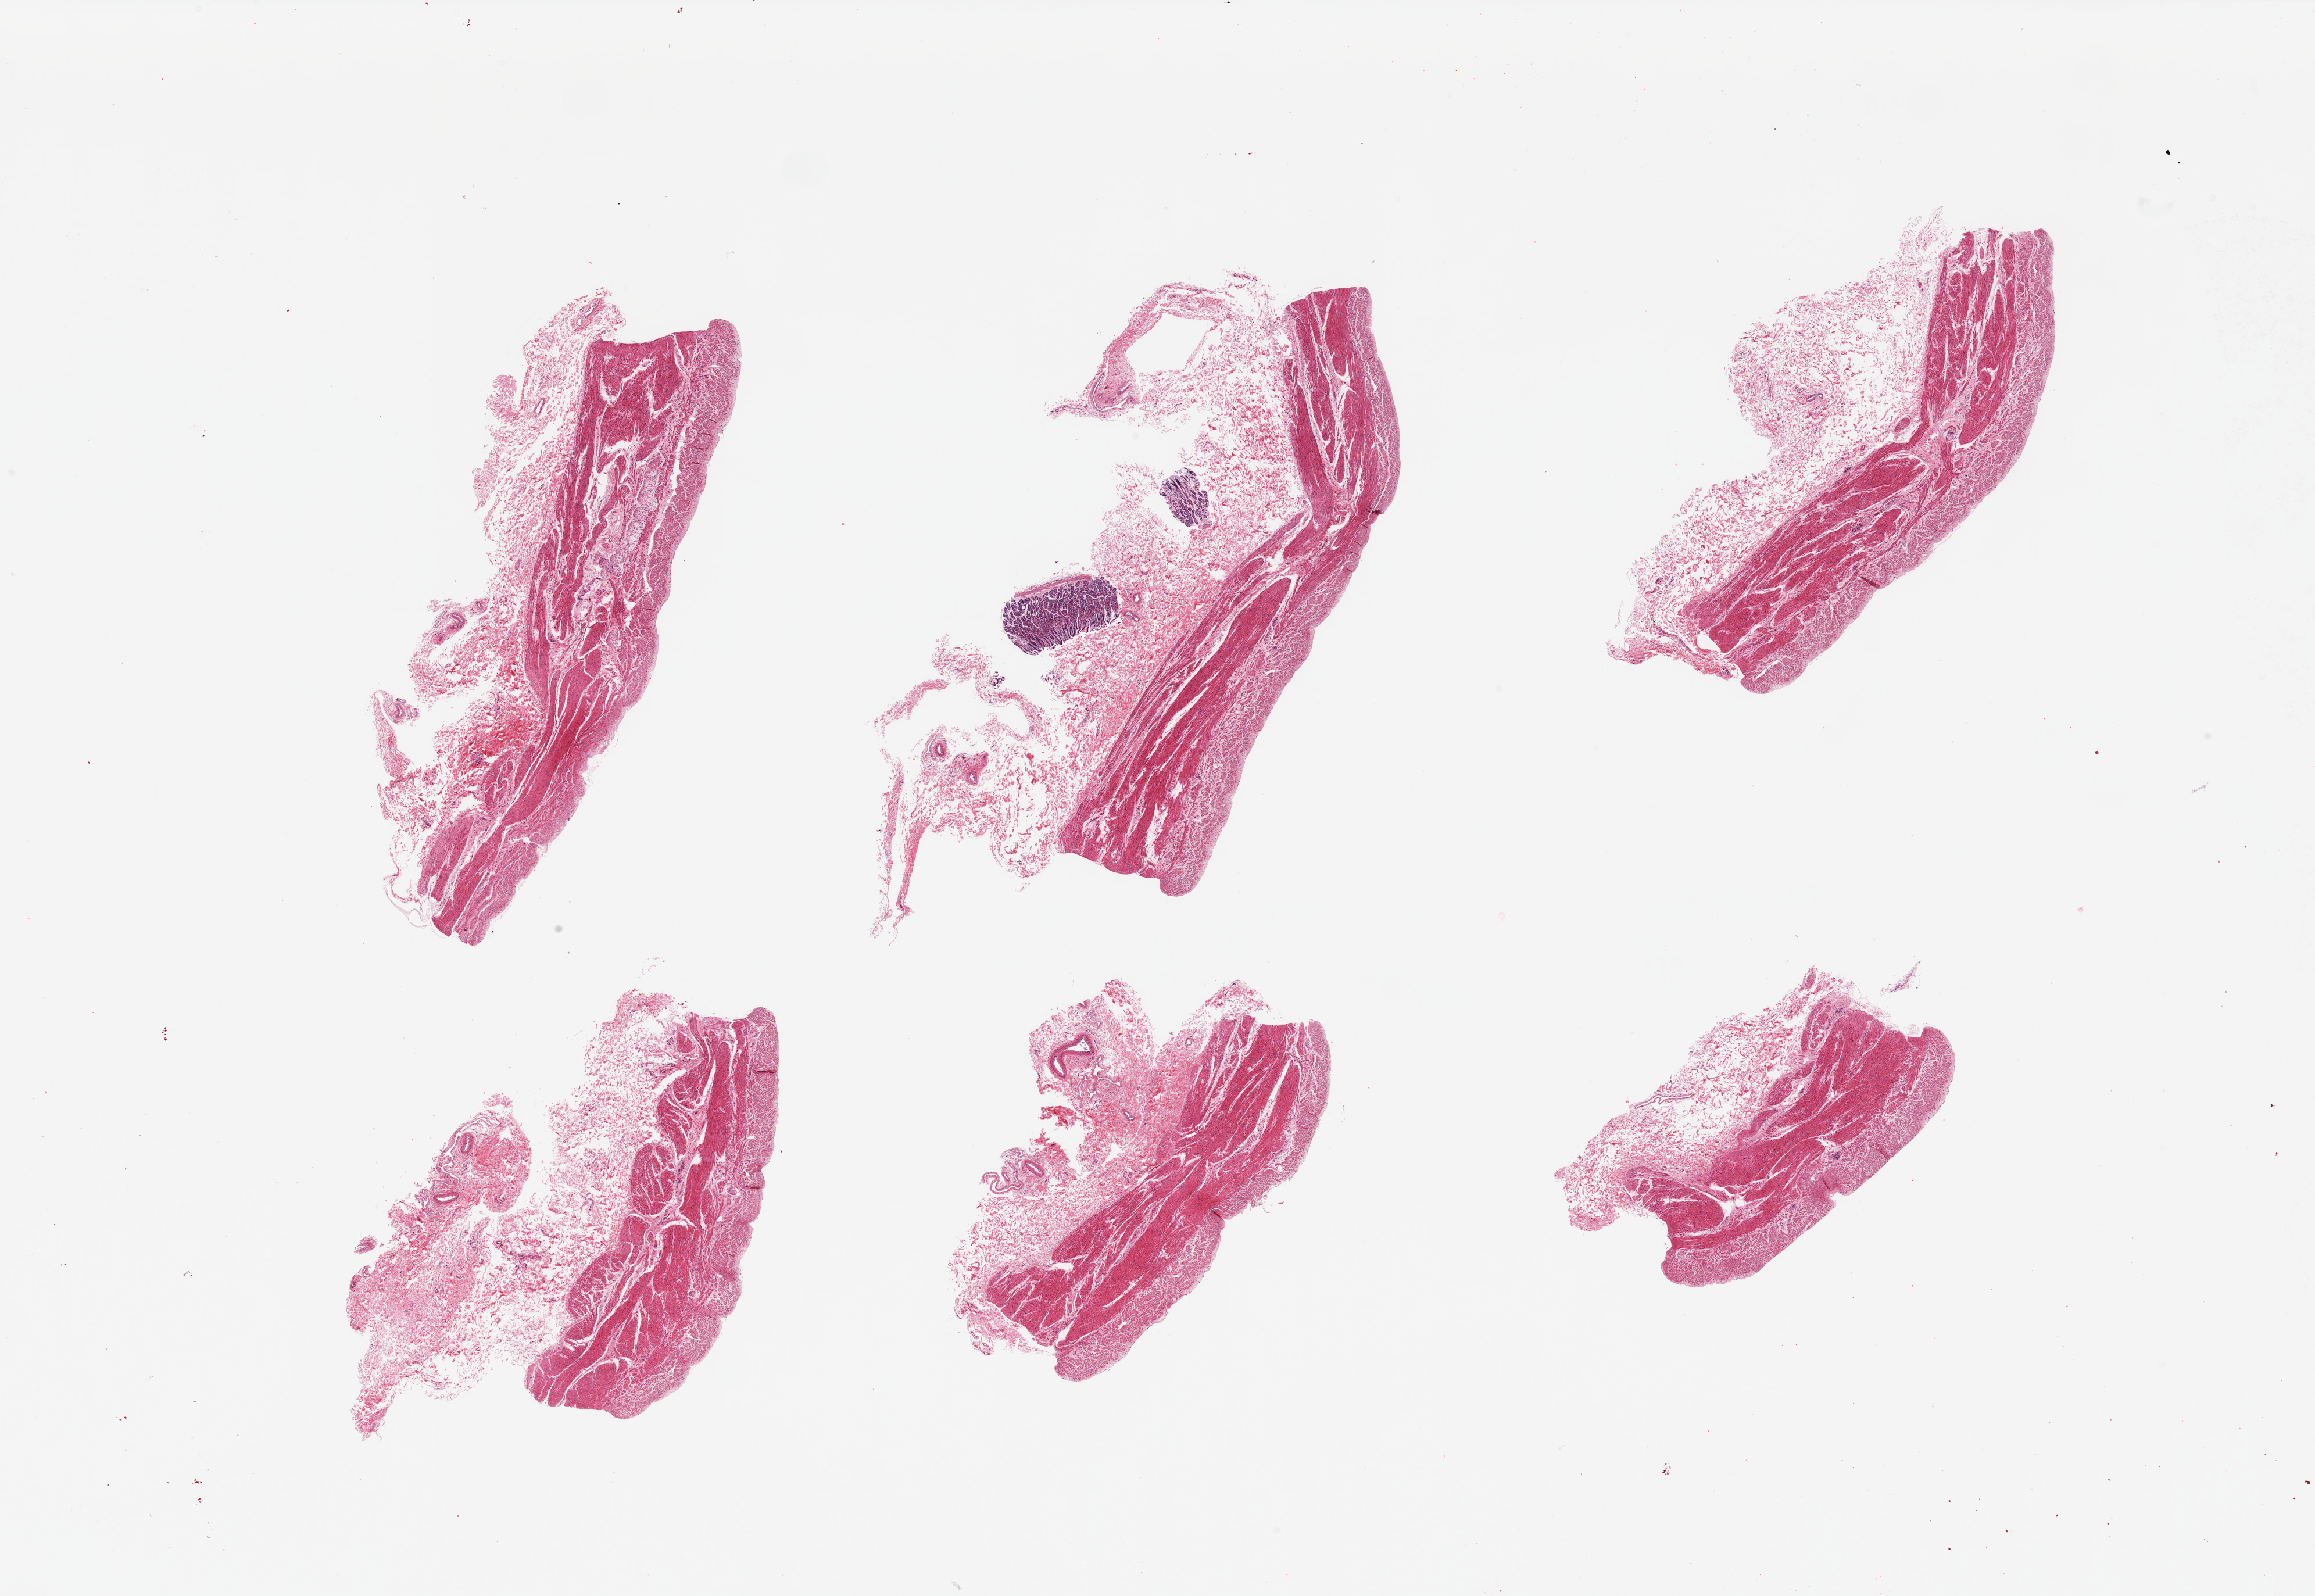
Hematoxylin and eosin (H&E) whole-slide image — whole scanned area (about 31.5 x 21.7 mm) shown as a low-resolution overview, PAXgene-fixed, paraffin-embedded tissue, sampled site (target tissue): stomach, donor tissue sample. Donor: male.
Review note (as recorded): 6 pieces; muscularis with few strips of residual mucosa.